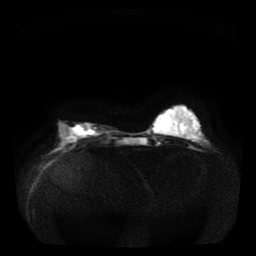
Breast MRI, one axial slice; slice 12 of 36 in the series (ordered by position); diffusion-weighted series; image 2 of 4 stored at this slice position (different b-values; order by instance number); 1.5 T; 5 mm slice thickness; 256 × 256 image matrix, field of view 330 × 330 mm. Female patient.
Structures marked on this image (manually delineated by an expert):
- tumour on diffusion-weighted imaging: bounding box [x1, y1, x2, y2] px = [73, 124, 95, 136]